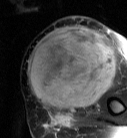
MRI of an extremity soft-tissue mass, one axial slice; slice 29 of 87 in the series (ordered by position); T2-weighted fat-saturated; MR volume resampled by the dataset authors to the PET/CT grid (not the native acquisition matrix); 3.27 mm slice thickness; 127 × 138 image matrix, field of view 124 × 135 mm. Female patient. Case-level facts recorded for this patient, not image findings: histological type: pleiomorphic leiomyosarcoma; grade: high; site of the primary tumour: left biceps.
Structures marked on this image (expert contour drawn on MRI and transferred to this co-registered scan by the dataset authors):
- gross tumour volume including surrounding oedema: bounding box (x1, y1, x2, y2) in pixels: (27, 27, 117, 113)
- gross tumour volume (mass): (27, 27, 117, 110)